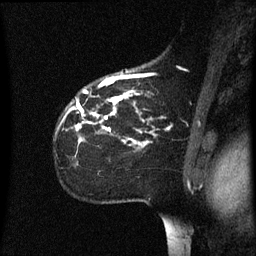
Breast MRI (dynamic contrast-enhanced), one sagittal slice. Slice 45 of 60 in the series (ordered by position). Dynamic contrast-enhanced series, image 2 of 3 at this slice position (ordered by acquisition). 1.5 T. TE 4.2 ms, TR 8.4 ms. 256 × 256 image matrix, field of view 200 × 200 mm. Patient: female, 35 years. Case-level facts recorded for this patient, not image findings: setting: breast cancer imaged before/during neoadjuvant chemotherapy; receptor status: HER2-positive.
Outlined on this slice (semi-automatic segmentation, software-assisted and operator-edited):
- analysis volume of interest (the breast-tissue region the enhancement analysis was run in; not a lesion): bounding box [x1, y1, x2, y2] px = [58, 78, 172, 163]
- tumour enhancement mask (voxels above the 70 % enhancement threshold inside the analysis volume of interest): [76, 94, 149, 145]